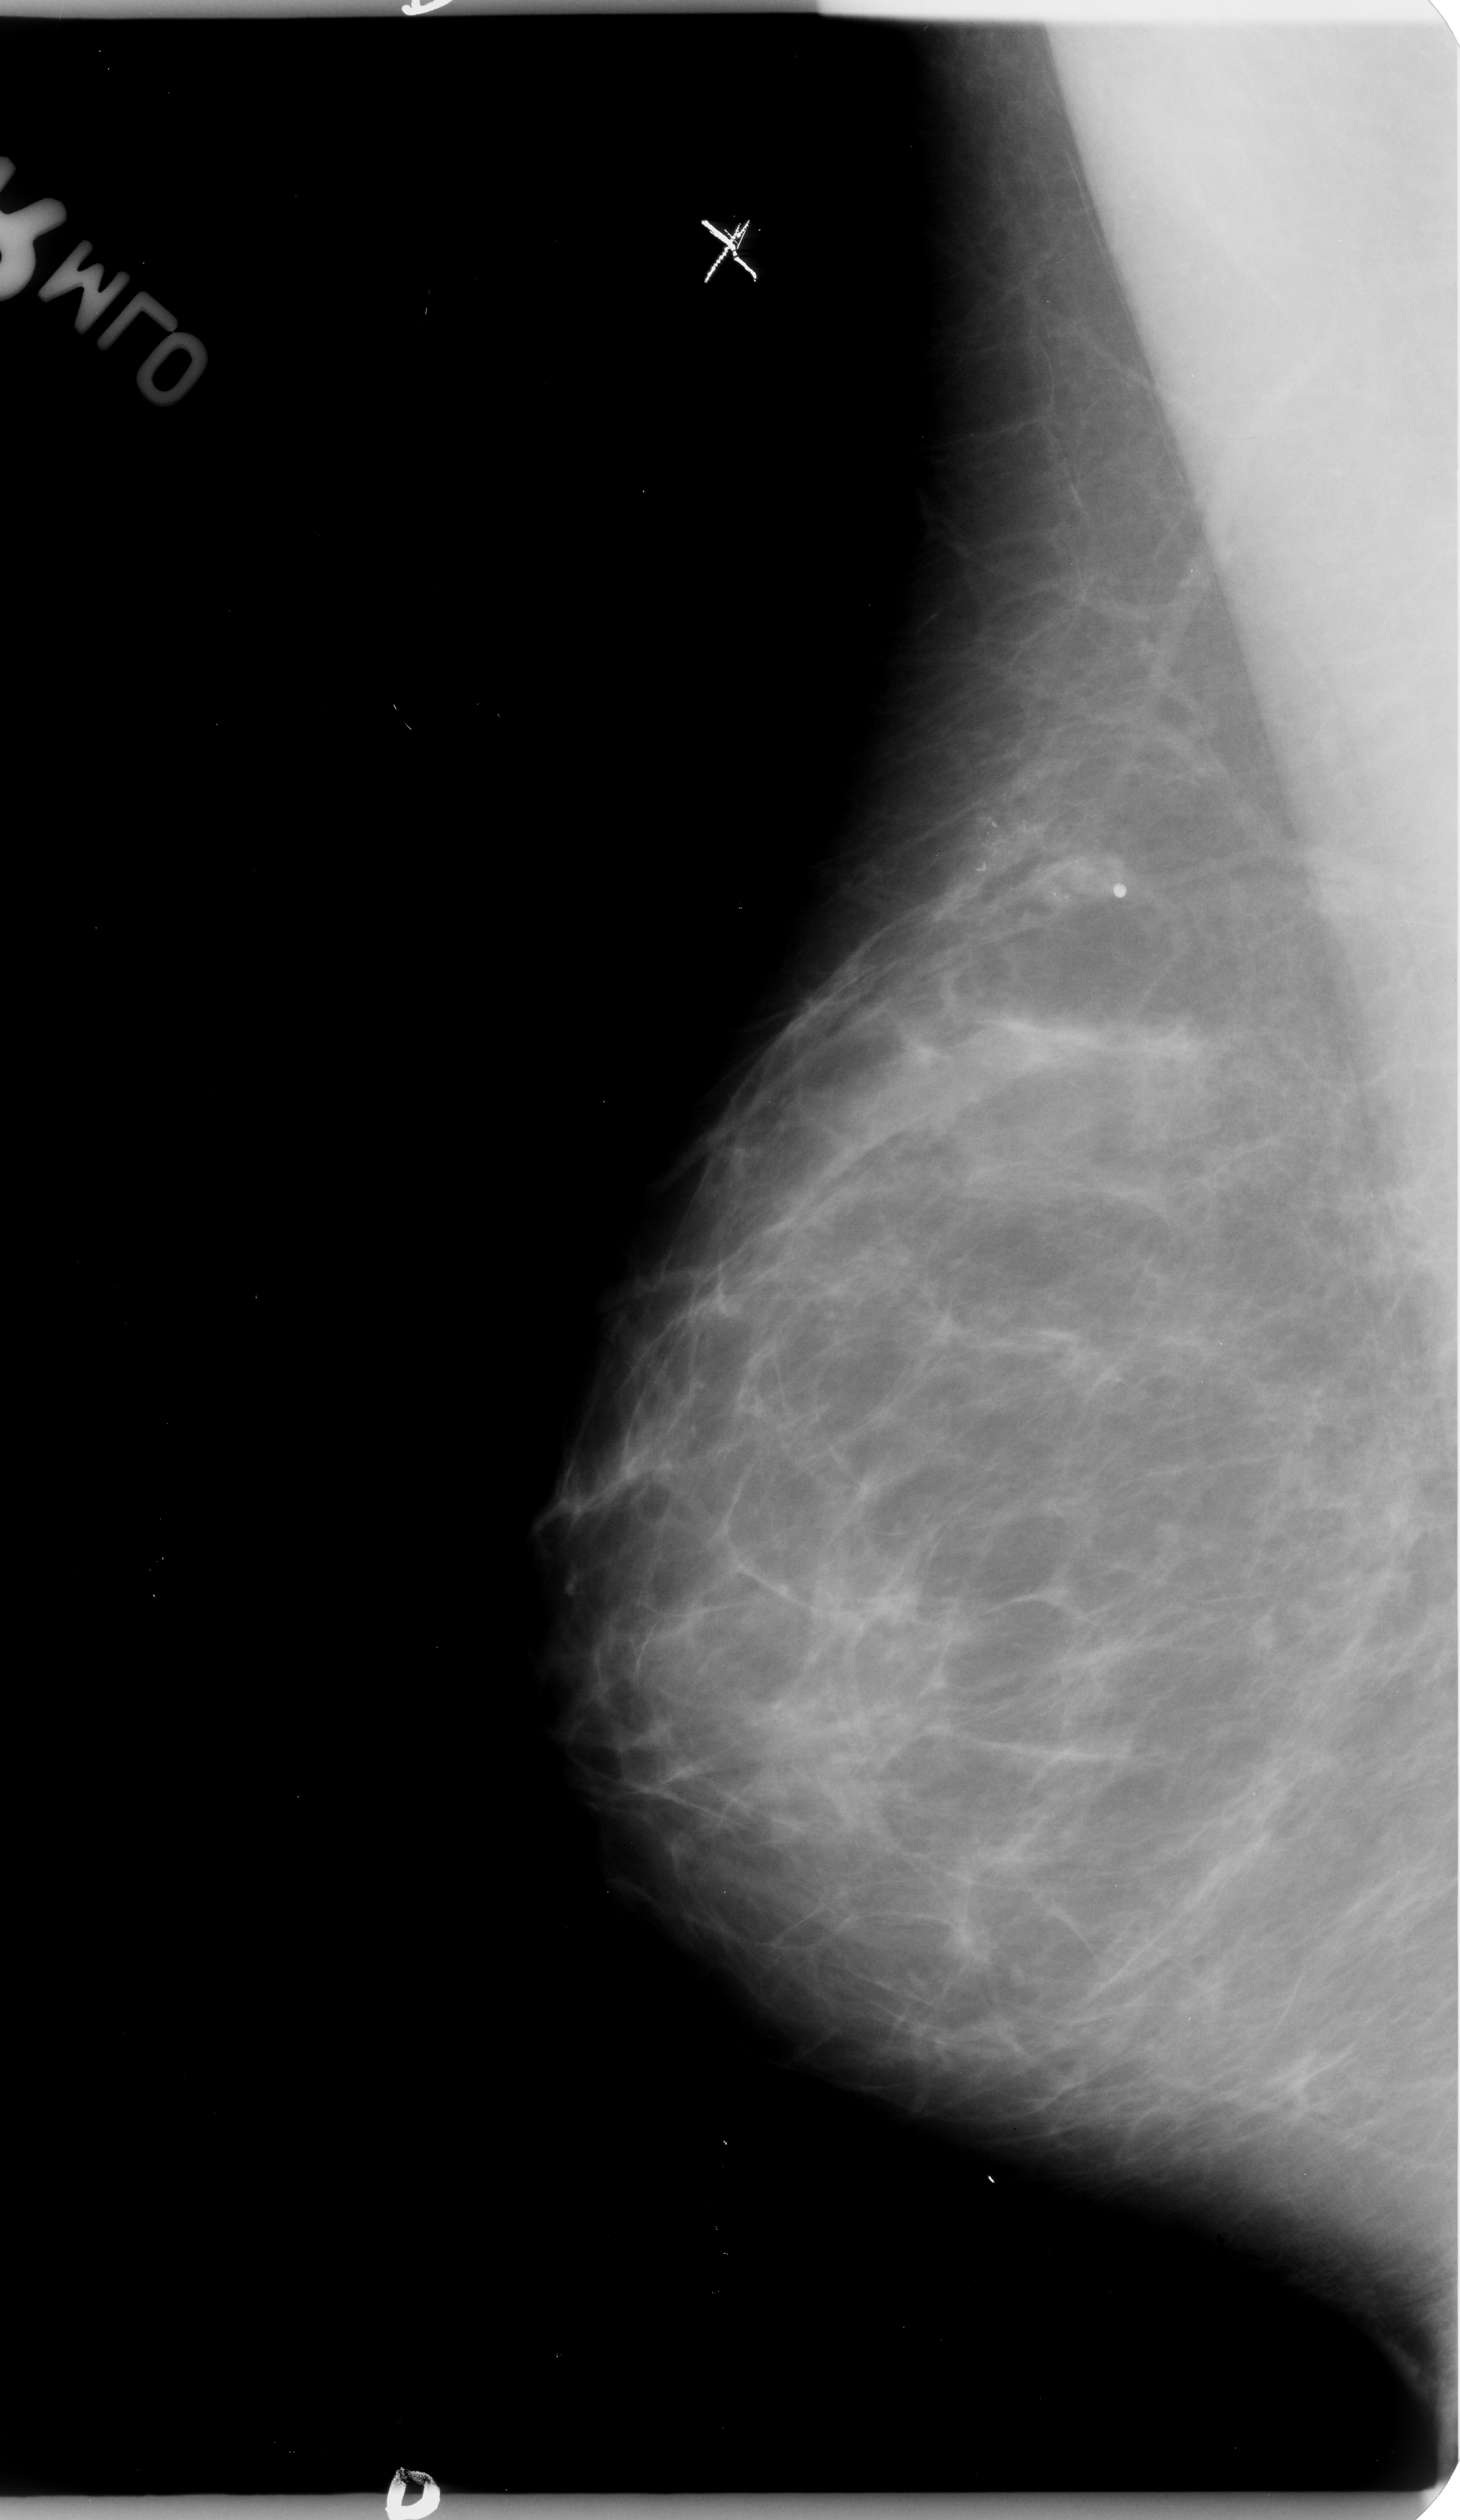
Mammogram (digitized film). Right breast. MLO view. 1460 × 2520 image matrix.
Marked abnormalities (boxes around the expert regions of interest):
- calcifications, morphology pleomorphic, distribution clustered; BI-RADS assessment category 4; pathology result (as recorded, not read from the image): malignant: box from (x=943, y=784) to (x=1065, y=914) px